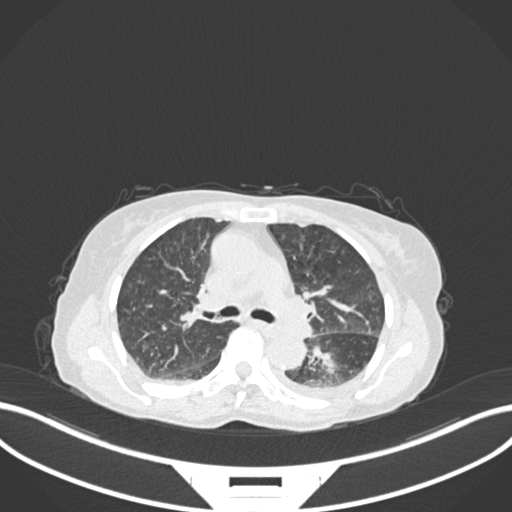
Chest CT, one axial slice. Slice 111 of 233 in the series (ordered by position). Reconstruction kernel B30f. Lung window (W 1500 / L -600 HU). 512 × 512 image matrix, field of view 400 × 400 mm. Female patient, age 78 years. From the clinical record (not read from this slice): clinical TNM (as recorded): T3 N0 M1.
Outlined on this slice (bounding box drawn by a radiologist):
- lung tumour (recorded histology: squamous cell carcinoma): bounding box <302,336,351,395> (left, top, right, bottom; pixels)